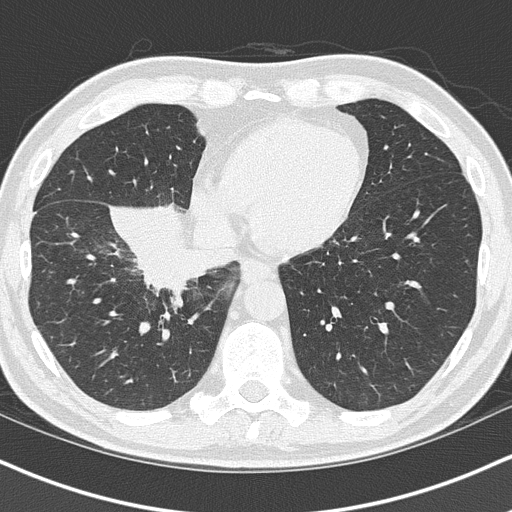
Low-dose screening chest CT, axial slice, baseline screening round, lung window (W 1500 / L -600 HU), 2 mm slice thickness, lung (sharp) reconstruction kernel (B50f), slice 39 of 151 in the series. Male participant, aged 55 years at enrolment. Current smoker at enrolment.
• Expert-annotated lung lesion, bounding box (x1, y1, x2, y2) in pixels: (119, 222, 244, 317).
• Screening reader's record for this exam (one nodule recorded; not confirmed to be the boxed lesion): non-calcified nodule or mass ≥4 mm, right lower lobe, 6 × 5 mm, spiculated (stellate) margins, soft tissue attenuation.
• Official screen result: positive, change unspecified: nodule(s) >= 4 mm or enlarging nodule(s), mass(es), or other non-specific abnormalities suspicious for lung cancer.
• Lung cancer was diagnosed 21 days after this screen: carcinoma, NOS, right hilum, stage IB (AJCC 6th edition), 67 mm at pathology.